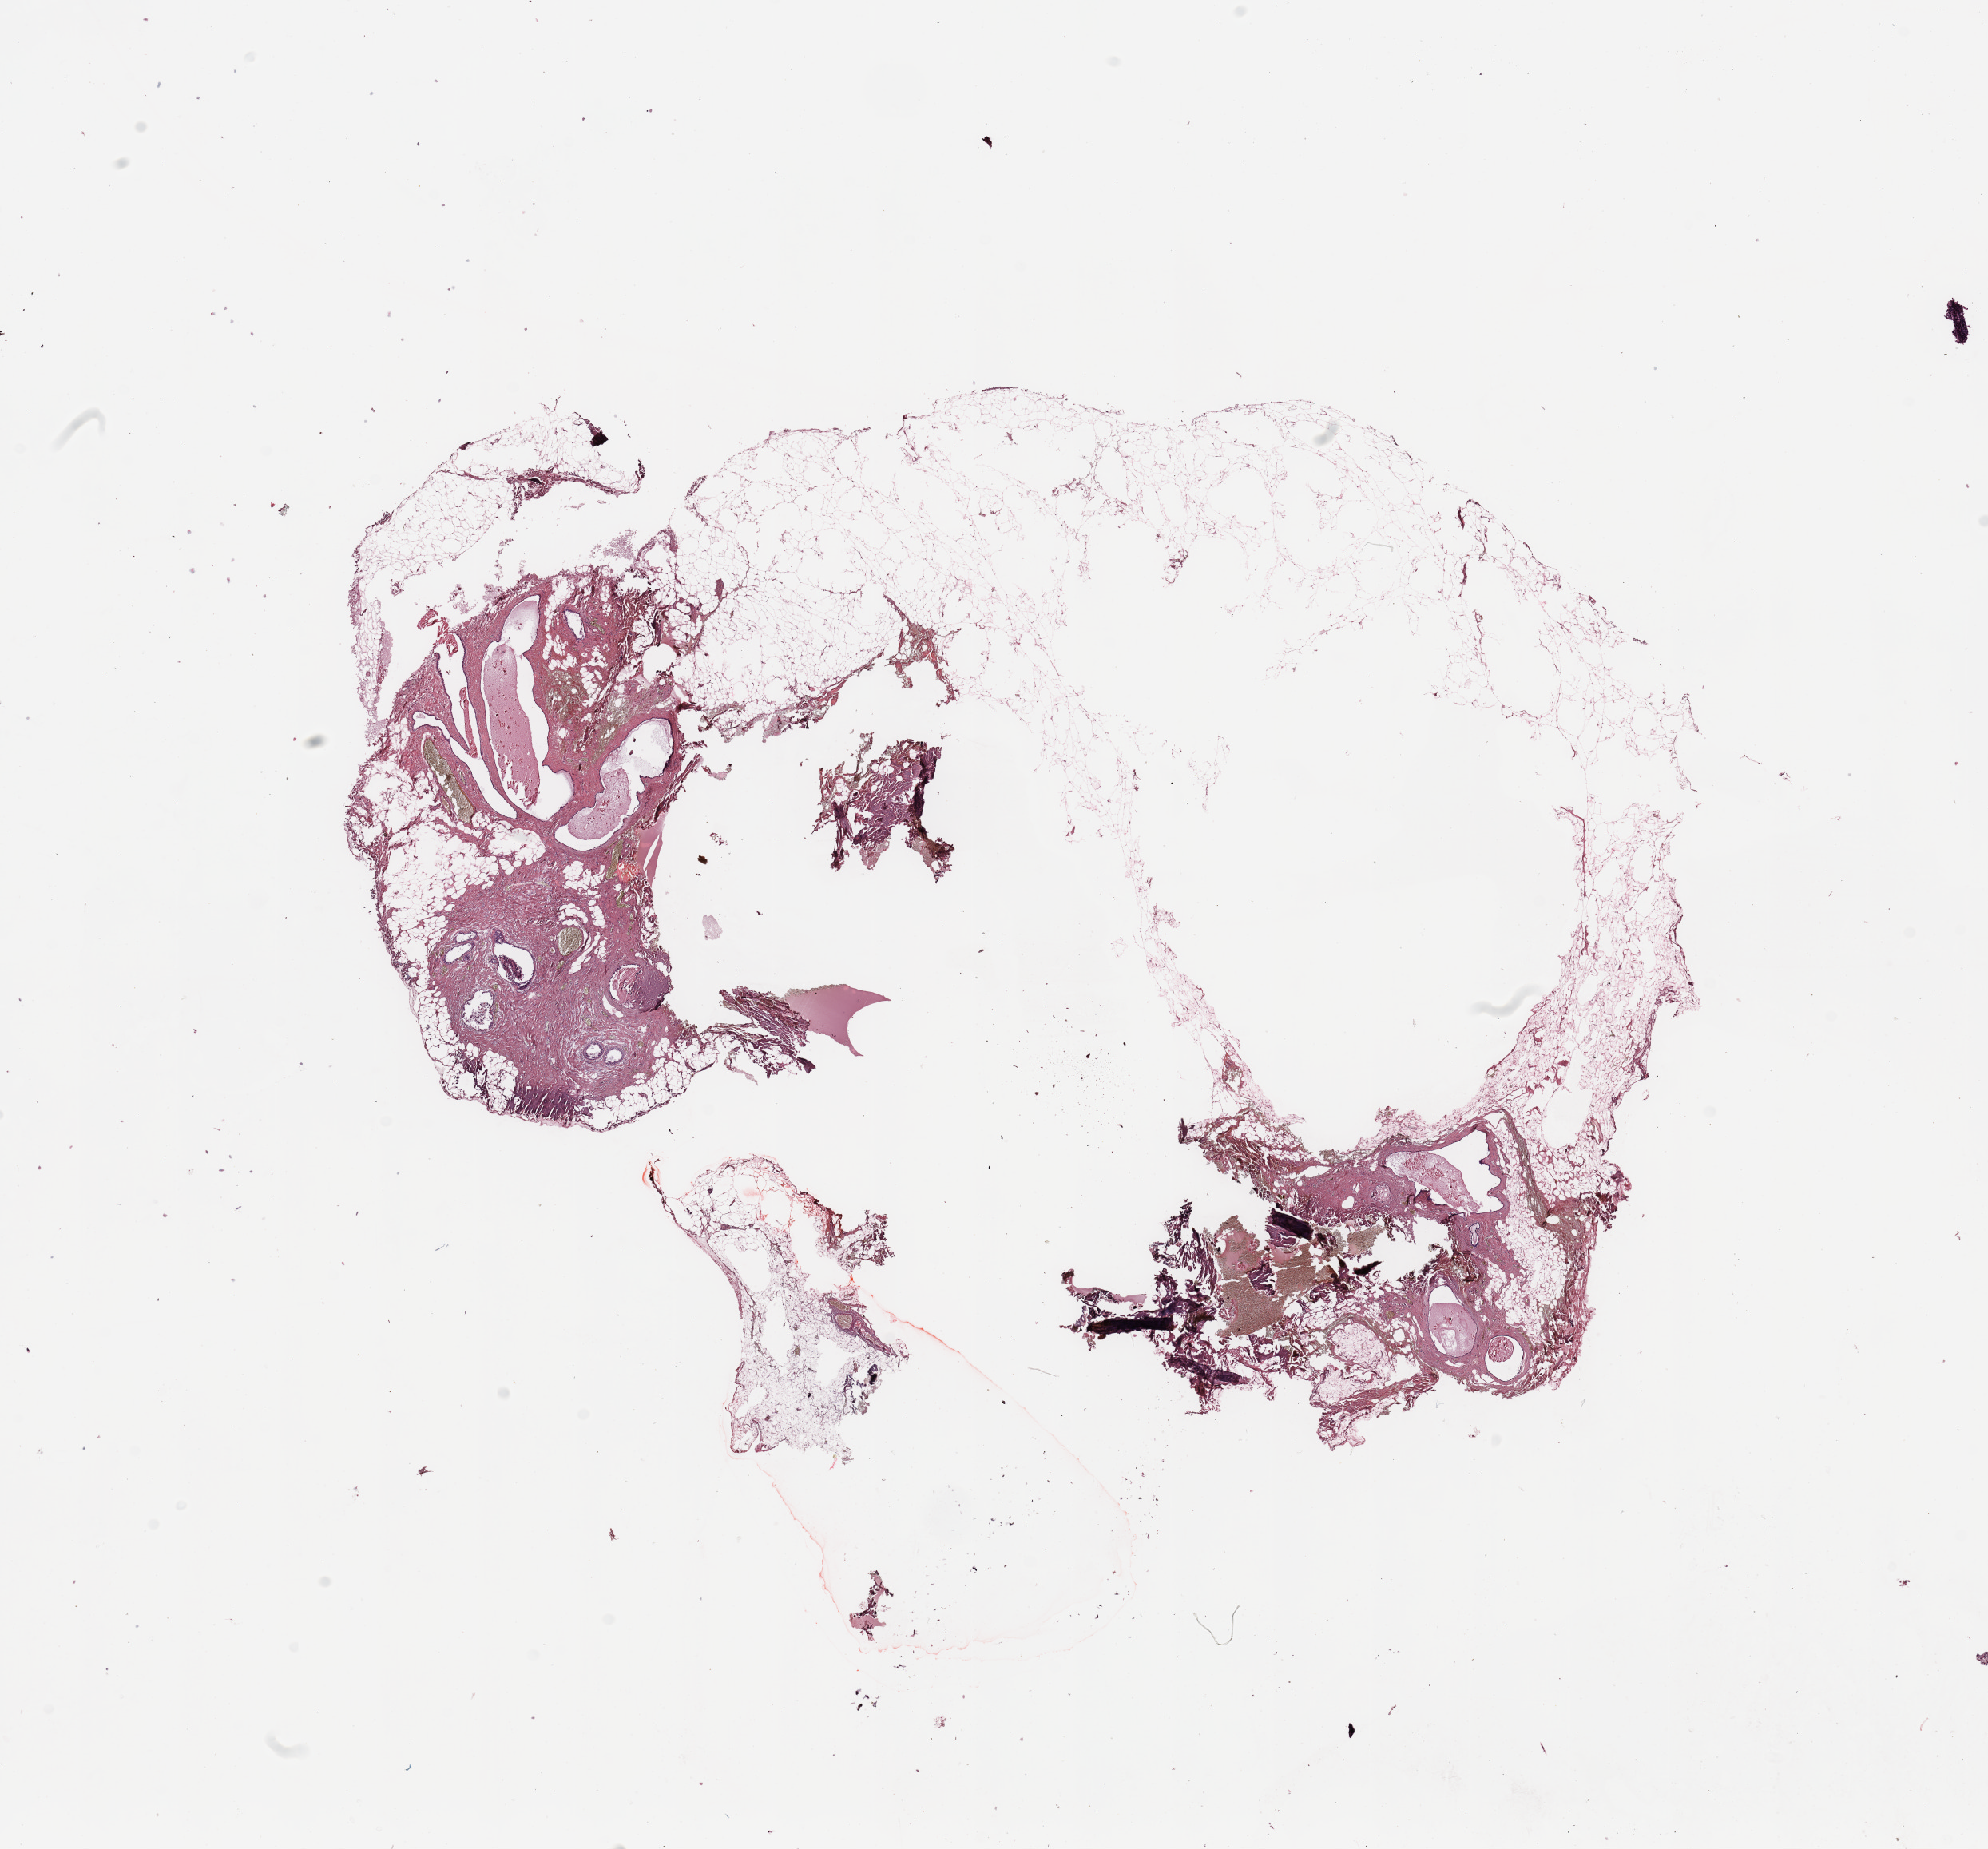
Whole-slide histology image, H&E, whole scanned area (about 19.7 x 18.3 mm, slide scanned at 20x) shown as a low-resolution overview, normal (non-tumour) tissue (melanoma cohort); sampled site not recorded. Patient: female, age 44 years.
This section: normal (non-tumour) tissue from the same patient. Patient diagnosis (cohort enrolment): cutaneous melanoma (skin).